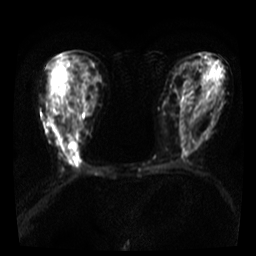
Breast MRI, one axial slice; position 15 of 36 along the scan axis; diffusion-weighted series; image 2 of 4 stored at this slice position (different b-values; order by instance number); 3 T; 5 mm slice thickness; 256 × 256 image matrix, field of view 300 × 300 mm. Female patient.
Annotated regions visible in this slice (manually delineated by an expert):
- tumour on diffusion-weighted imaging: box from (x=69, y=143) to (x=77, y=151) px